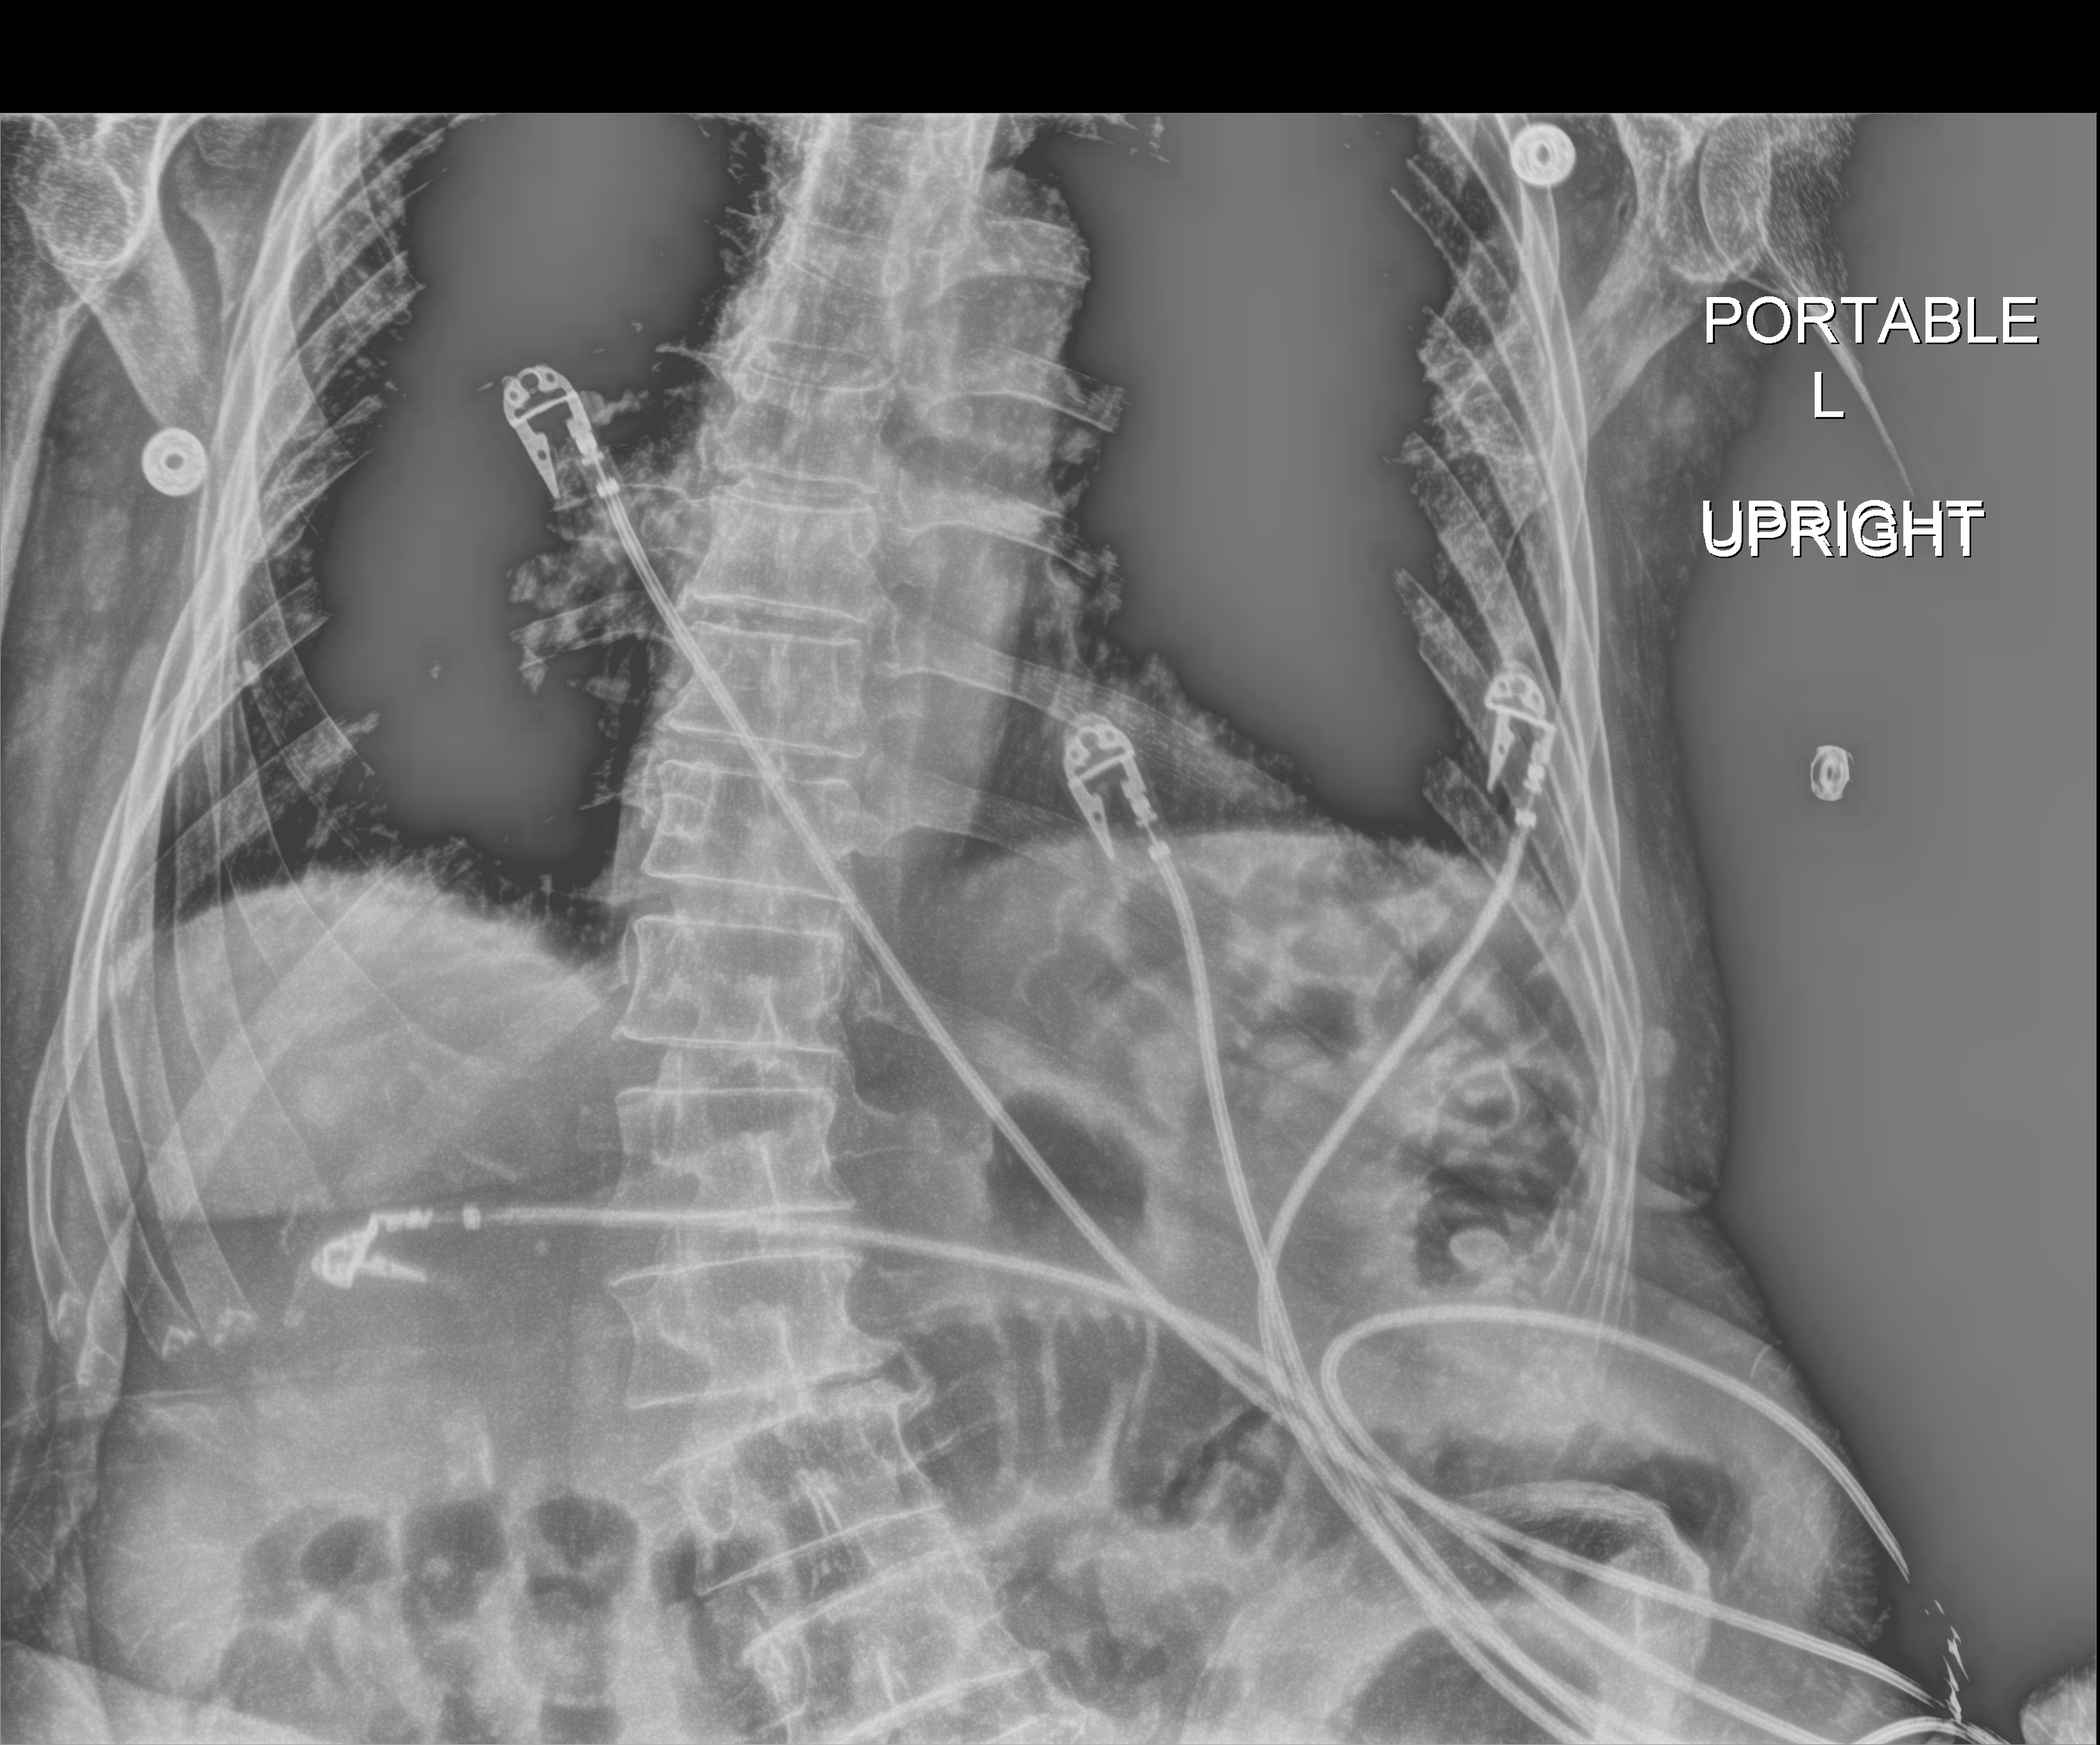
Bedside abdomen radiograph (digital radiography); anteroposterior (AP) projection. Male patient hospitalised with COVID-19, age 75–90 years.
Admission-level facts for this patient (not findings on this image; timing relative to this image not recorded):
- smoking status (admission record): never
- other chronic lung disease (admission record): yes
- hypertension (admission record): no